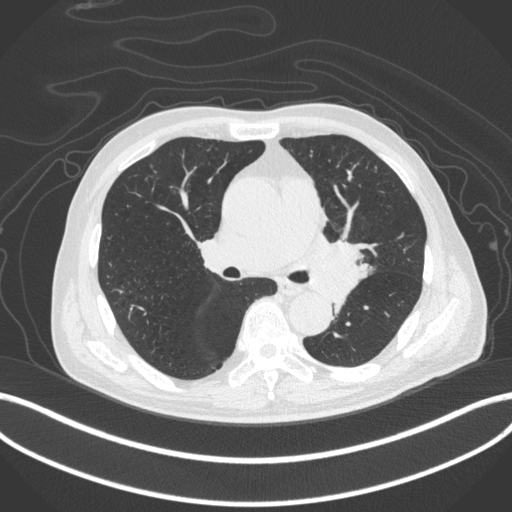
Chest CT, one axial slice. Reconstruction kernel B31f. Lung window (W 1500 / L -600 HU). 1 mm slice thickness. 512 × 512 image matrix, field of view 400 × 400 mm. Patient: male, 77 years. From the clinical record (not read from this slice): clinical TNM (as recorded): T3 N1 M0.
Annotated regions visible in this slice (rectangle marked by the reading radiologist):
- lung tumour (recorded histology: adenocarcinoma): box from (x=304, y=233) to (x=370, y=308) px